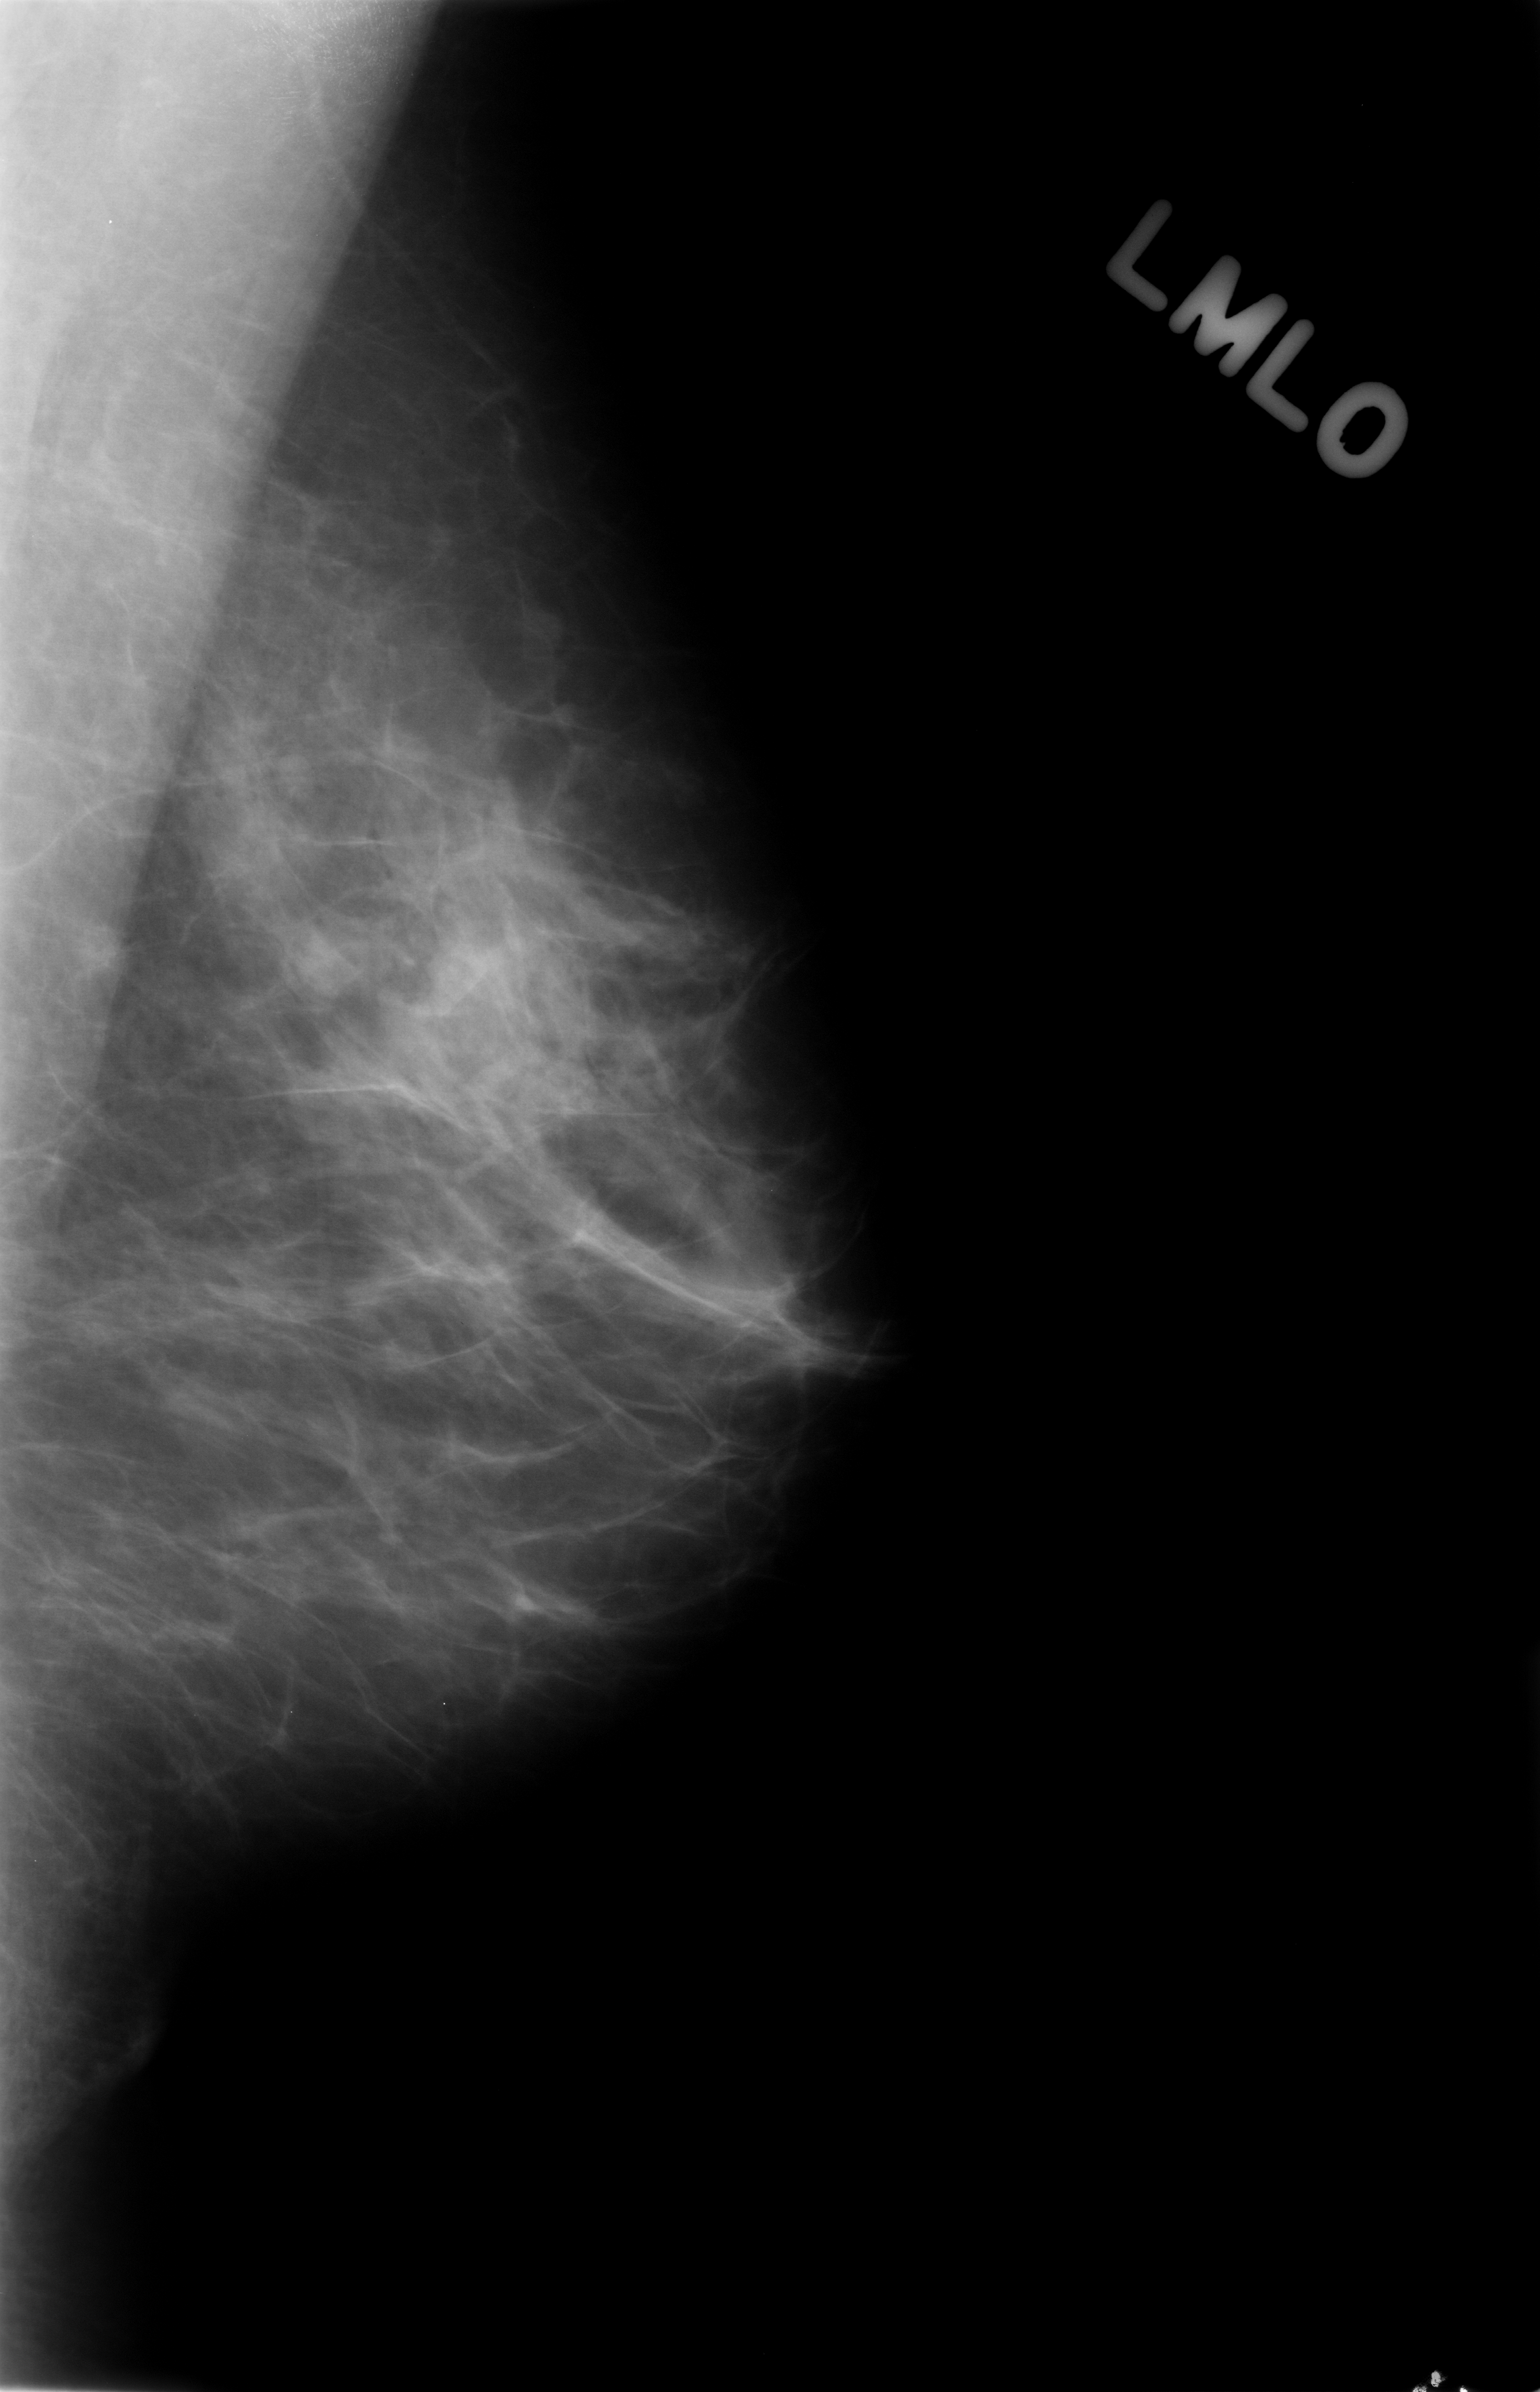
Scanned film-screen mammogram; left breast; mediolateral oblique (MLO) view; breast composition: scattered fibroglandular densities (BI-RADS density category 2 of 4).
Radiologist-marked abnormalities on this image: mass, shape asymmetric breast tissue; BI-RADS assessment category 3; benign; no additional work-up was recommended (benign without callback).